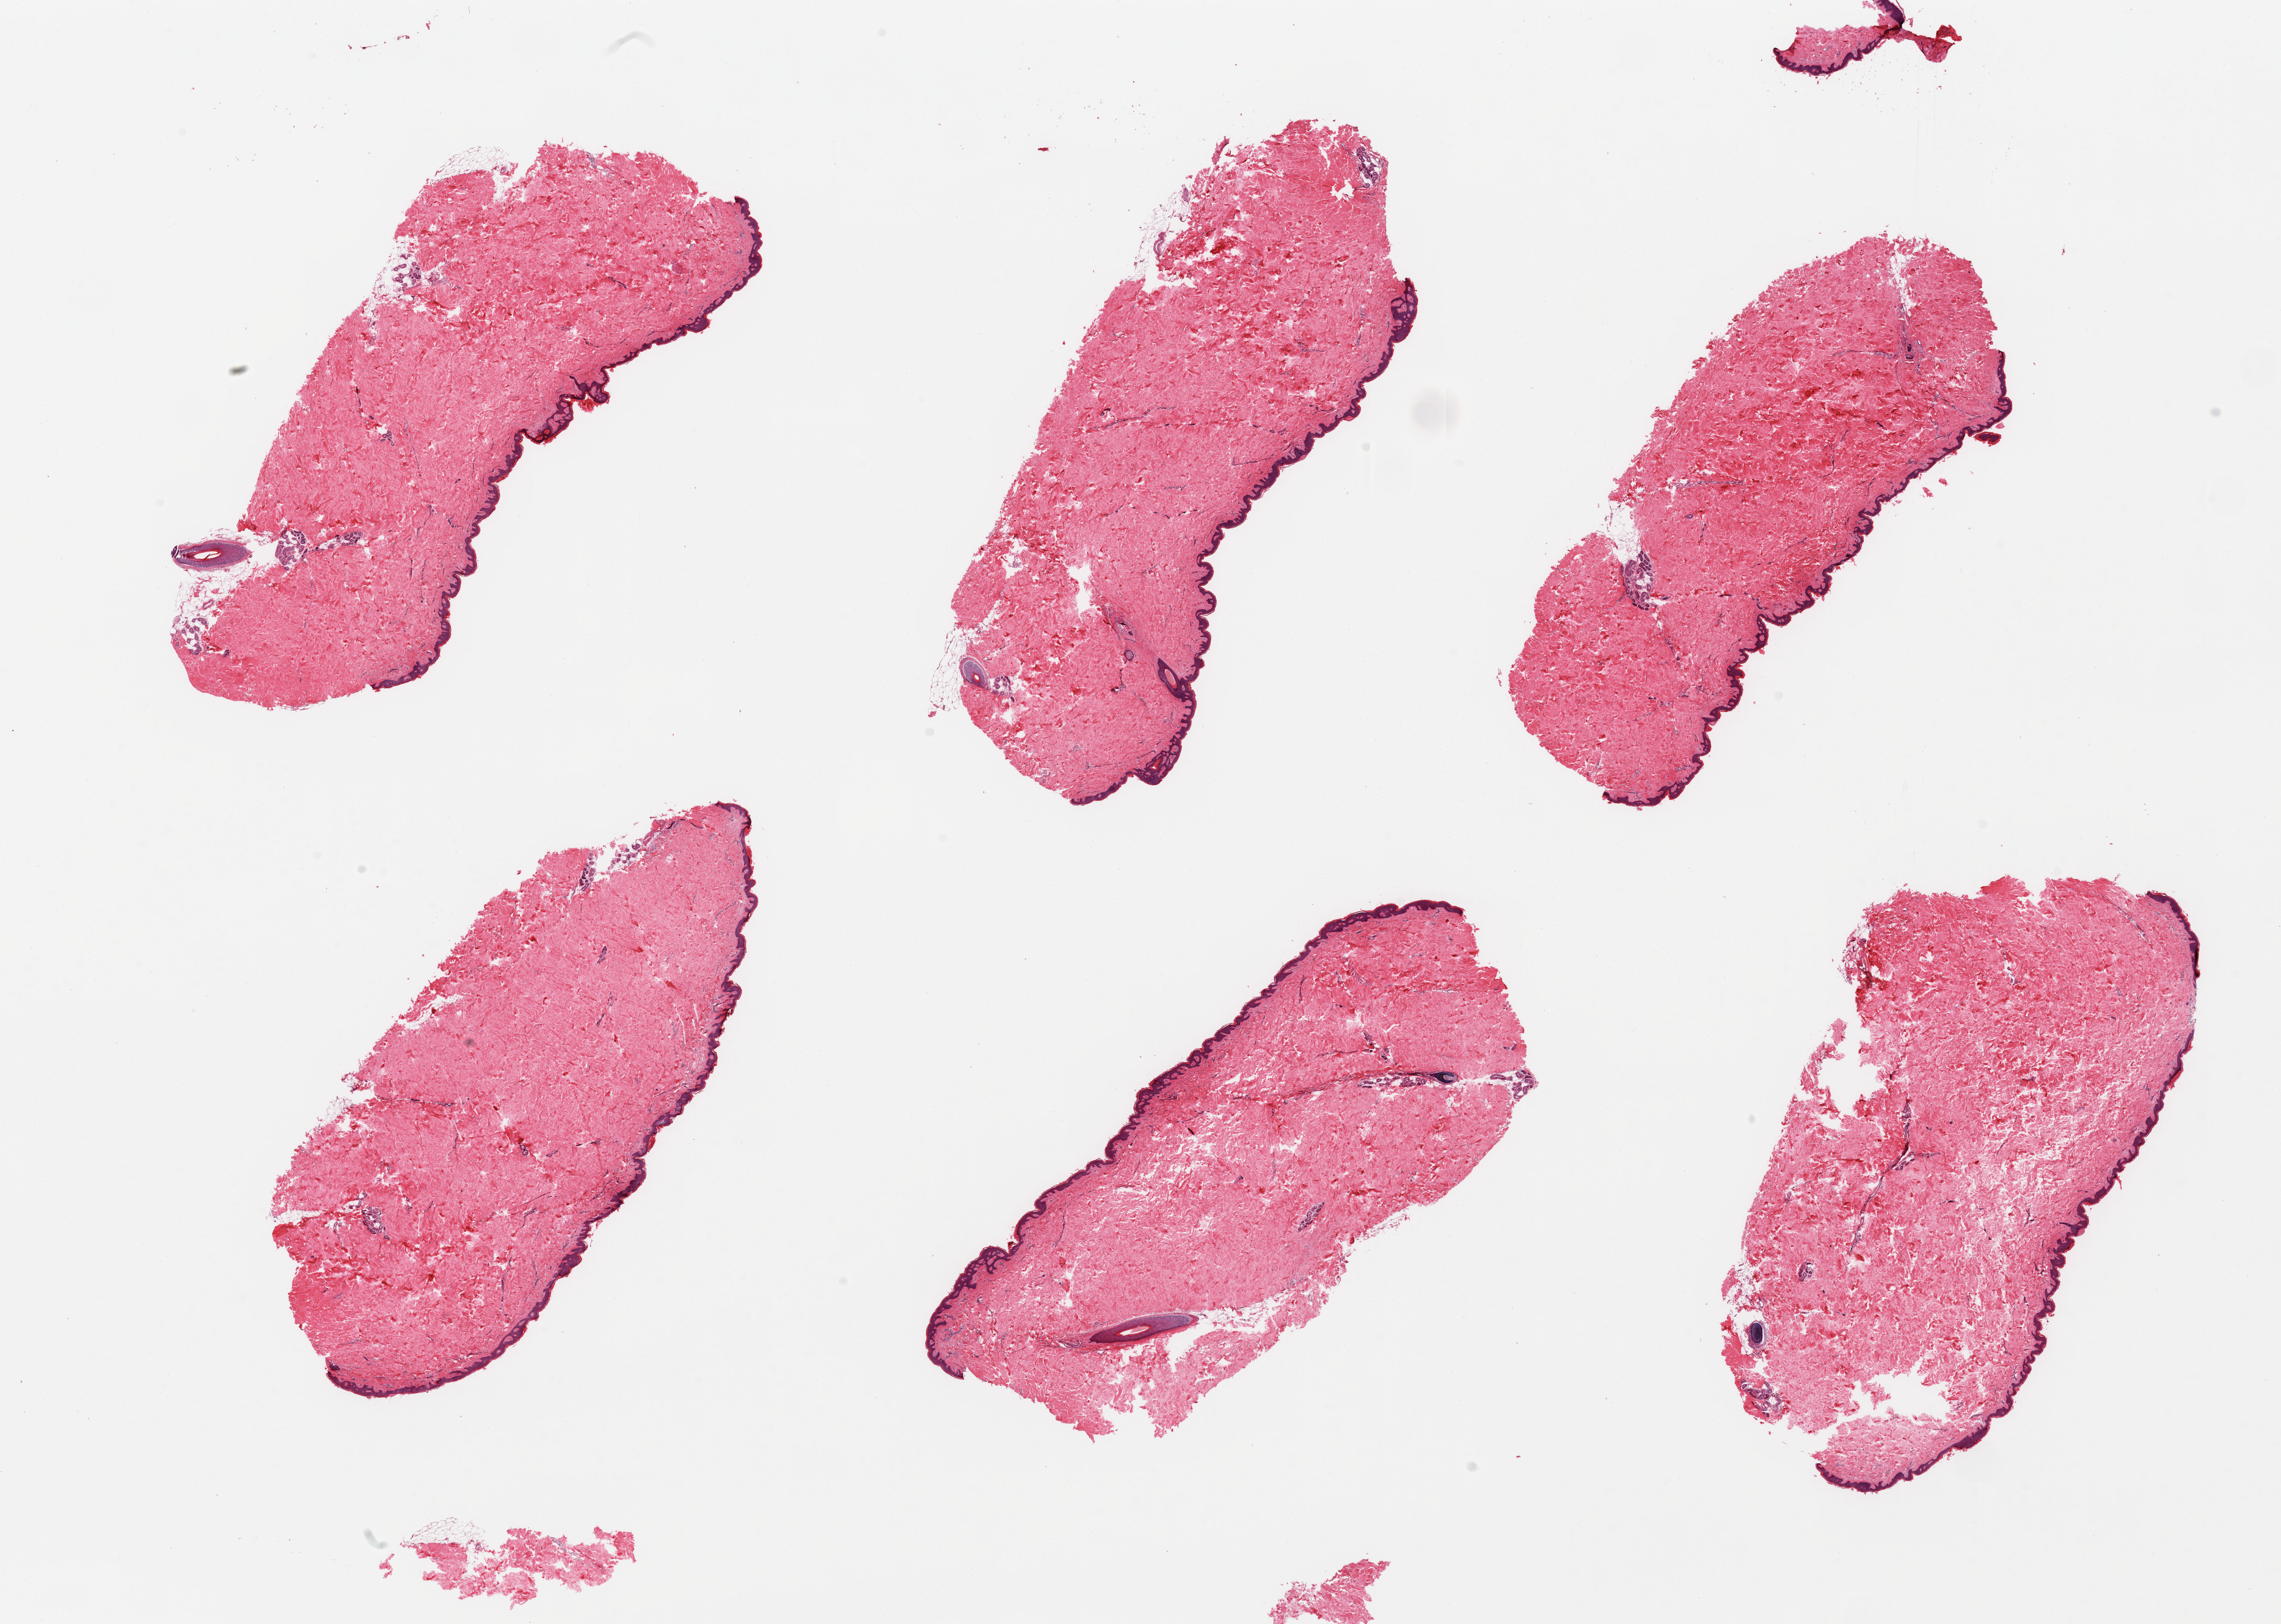
Hematoxylin and eosin (H&E) whole-slide image, a low-resolution overview of the entire scanned area, about 29.5 x 21.0 mm (slide scanned at 20x); PAXgene-fixed, paraffin-embedded tissue; sampled site (target tissue): skin of suprapubic region; tissue donor sample. Donor sex: male.
Pathologist's review note for this sample: 6 pieces; essentially well trimmed.